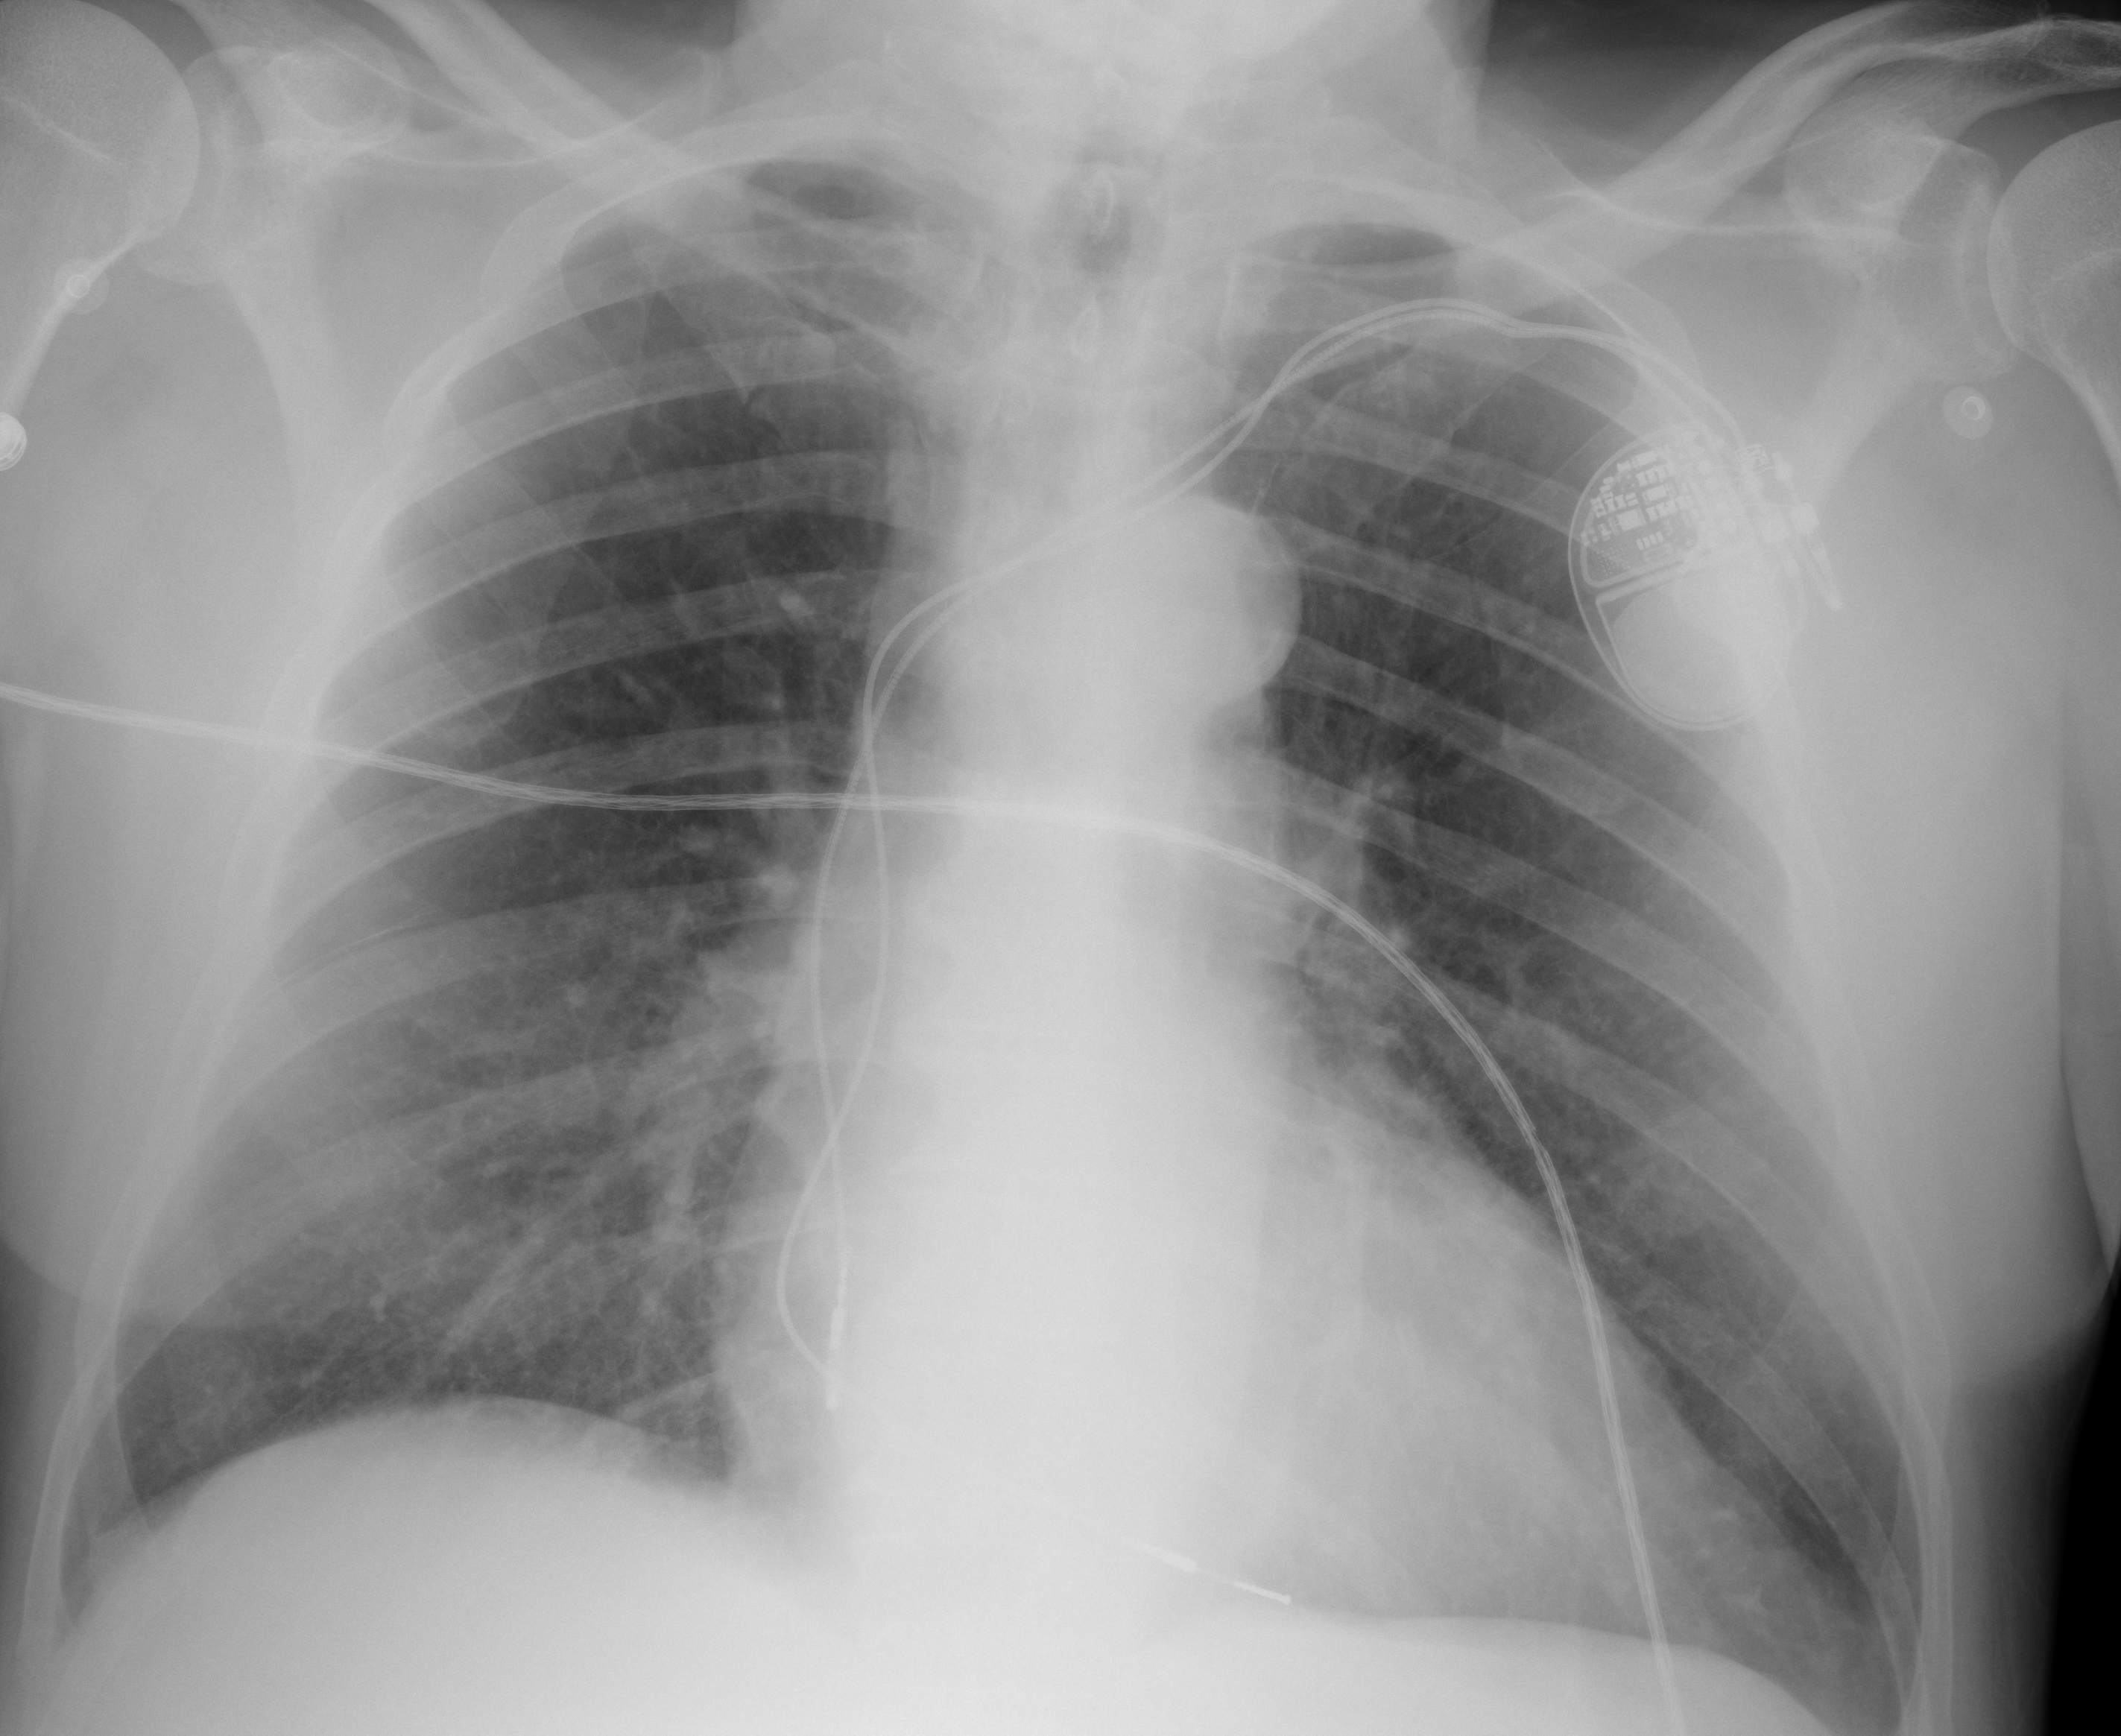
Chest X-ray (portable), AP projection. Male patient, age 79 years; imaged 18 days after the COVID-19 diagnosis.
Key findings recorded by the radiologist: Trace right basilar opacity felt to represent atelectatic changes.